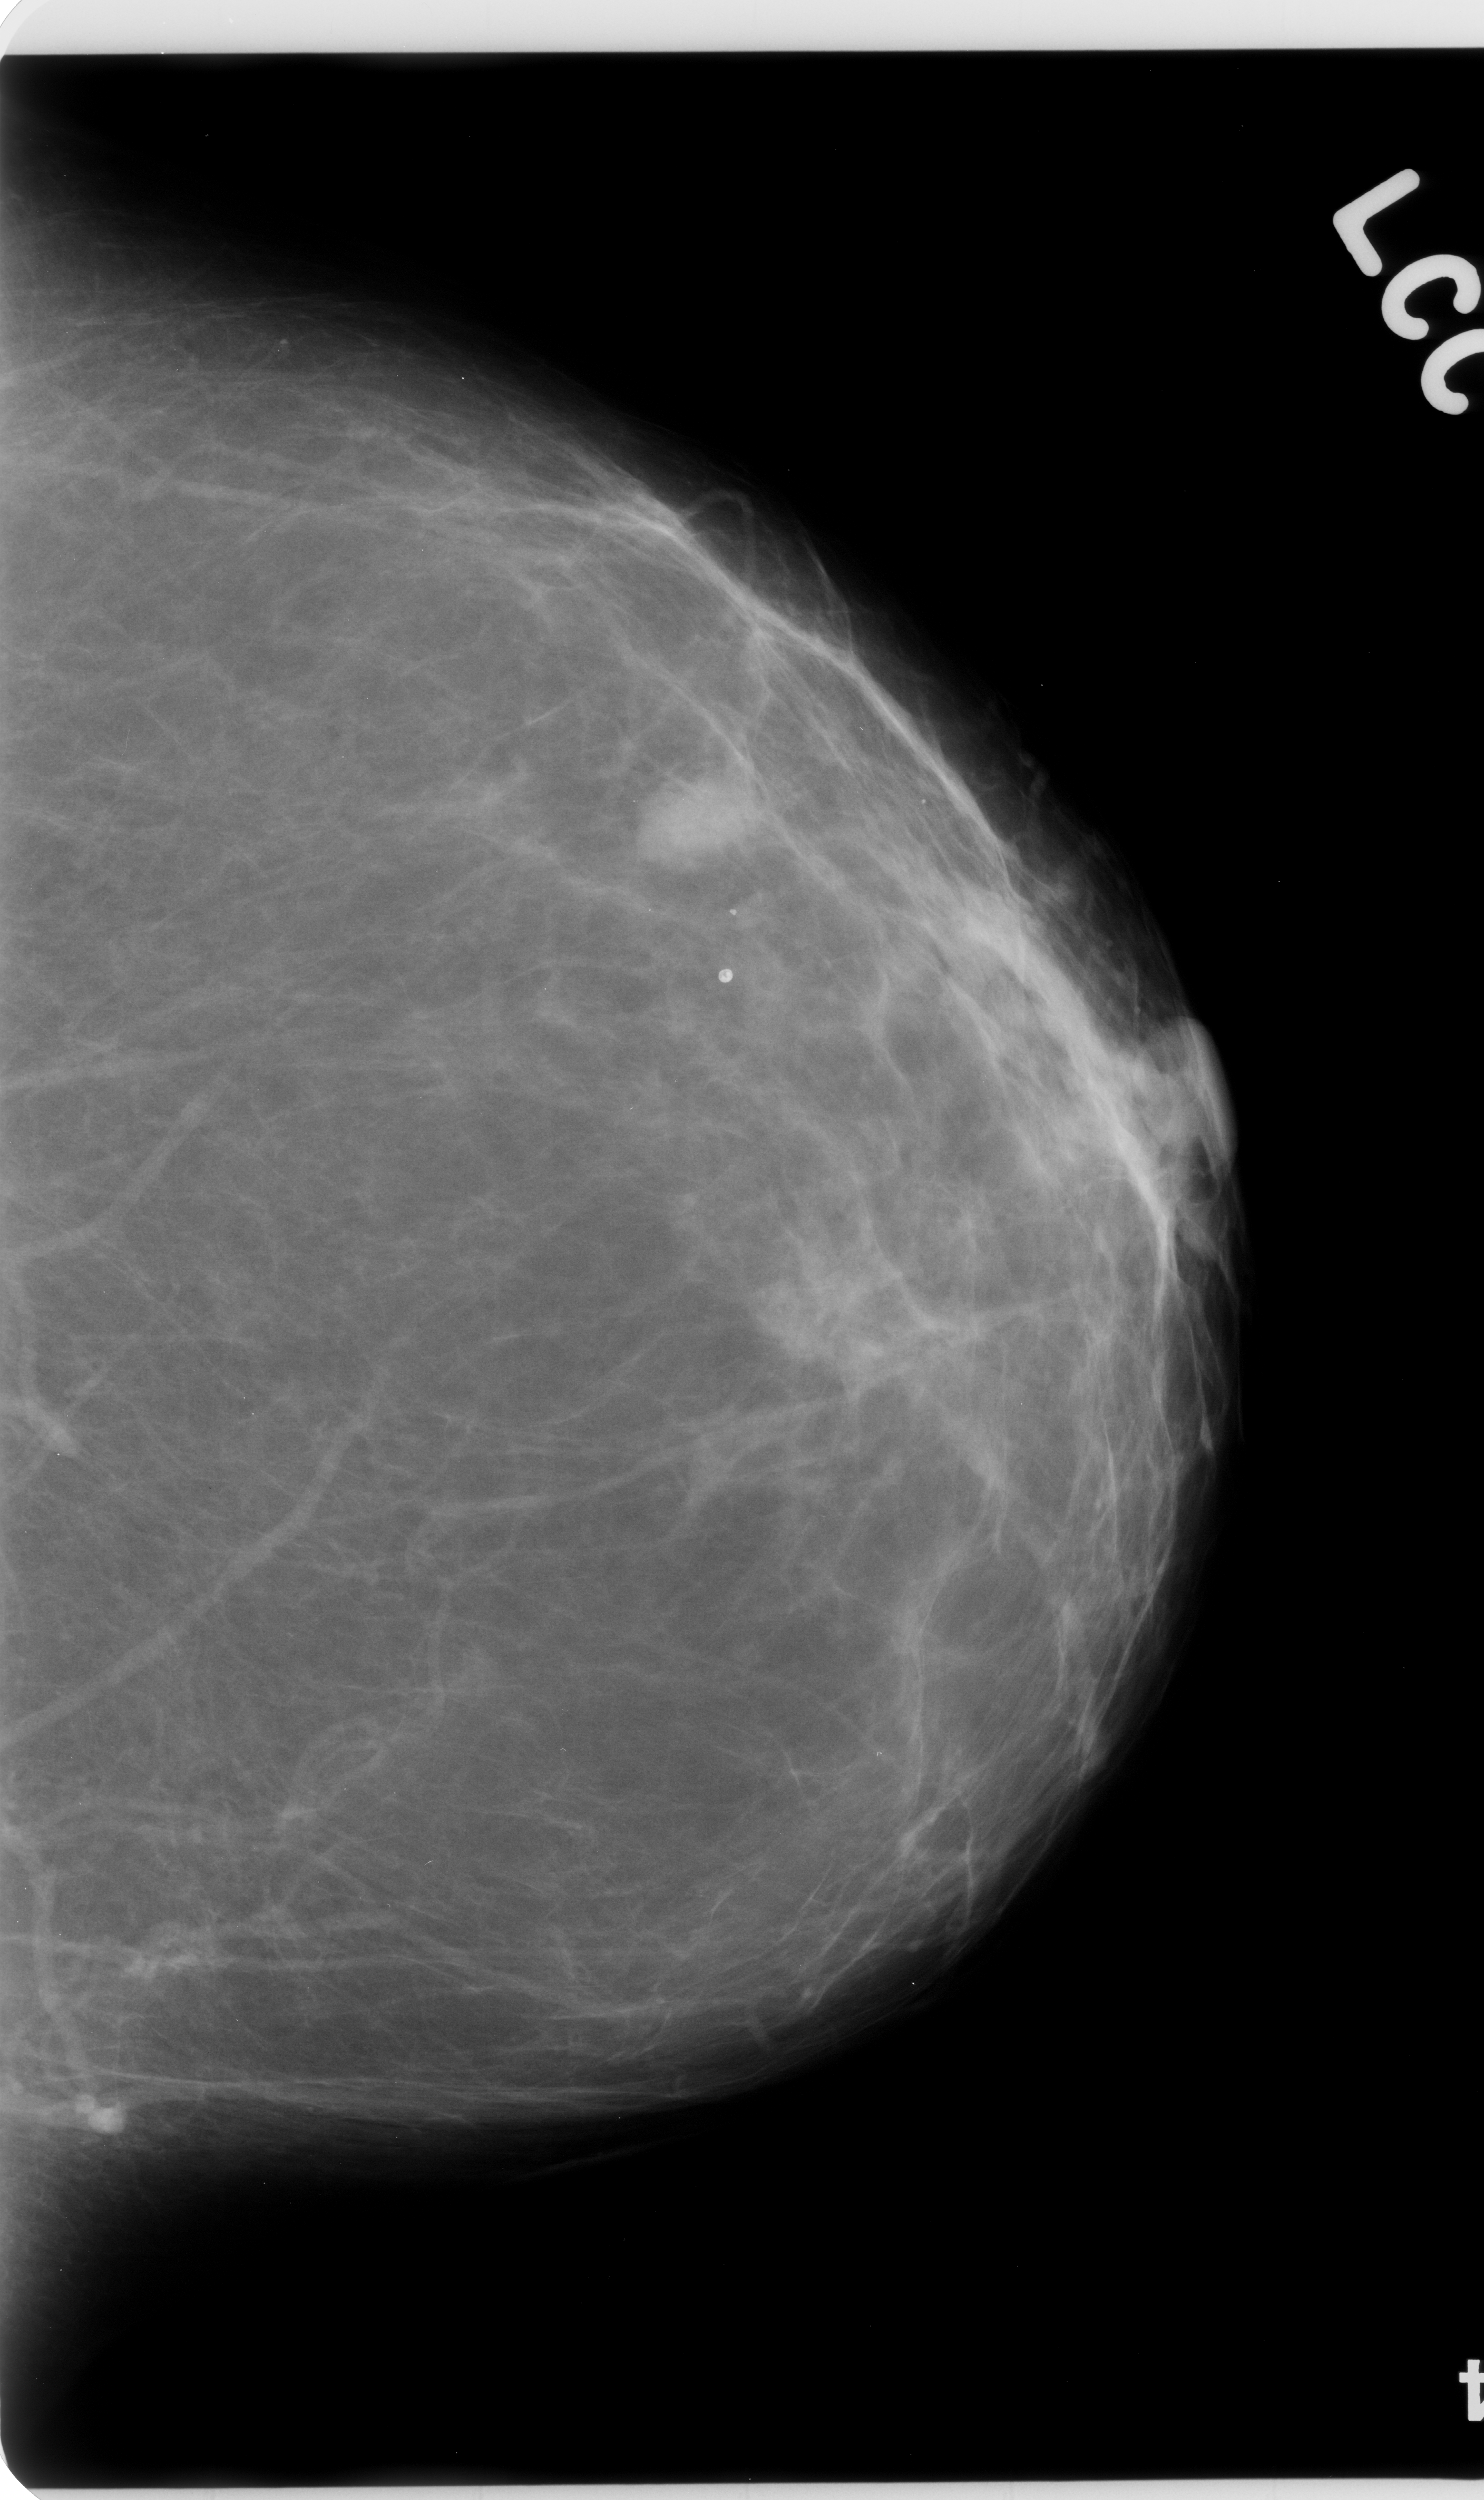
Mammogram (digitized film), left breast, CC view, breast composition: almost entirely fatty (BI-RADS density category 1 of 4).
Abnormality record for this image: mass, shape oval, margins microlobulated; BI-RADS assessment category 4; subtlety rating 5 on a 1 (subtle) to 5 (obvious) scale; pathology result (as recorded, not read from the image): malignant.